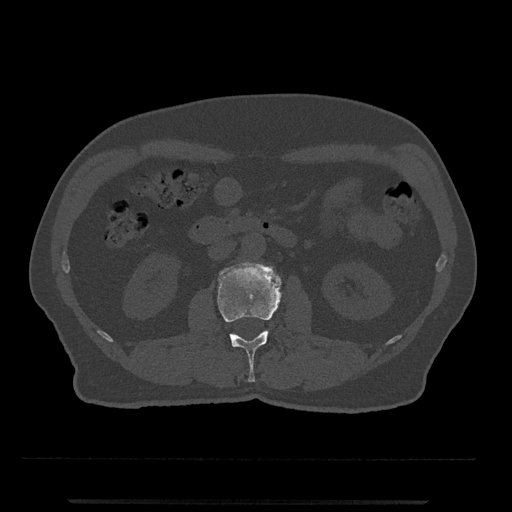
CT including the spine, one axial slice. Reconstruction kernel Br40s/3. 120 kVp. Bone window (W 1800 / L 400 HU). 512 × 512 image matrix, field of view 419 × 419 mm. Male patient, age 63 years. Case-level facts recorded for this patient, not image findings: primary cancer: prostate.
Structures marked on this image (semi-automatically segmented with operator editing):
- L2 vertebra: bounding box (x1, y1, x2, y2) in pixels: (217, 261, 281, 382)